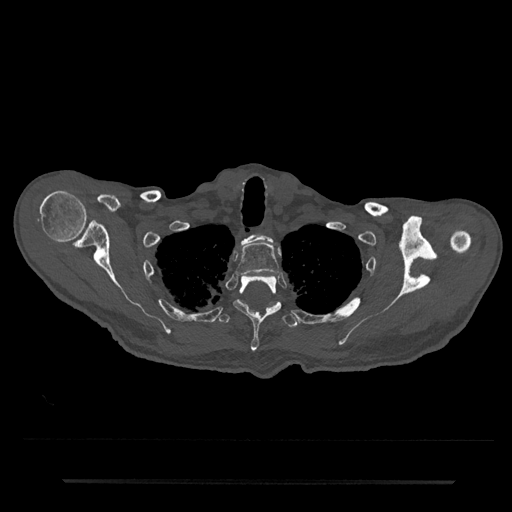
CT including the spine, one axial slice; slice 662 of 797 in the series (ordered by position); reconstruction kernel Br40s/3; 120 kVp; bone window (W 1800 / L 400 HU); 512 × 512 image matrix, field of view 427 × 427 mm. Patient: male, 74 years. From the clinical record (not read from this slice): primary cancer: prostate.
Annotated regions visible in this slice (semi-automatic segmentation, software-assisted and operator-edited):
- T1 vertebra: bounding box [x1, y1, x2, y2] px = [241, 234, 274, 244]
- T2 vertebra: [236, 243, 279, 276]
- T3 vertebra: [233, 275, 282, 352]
- T4 vertebra: [217, 301, 298, 329]